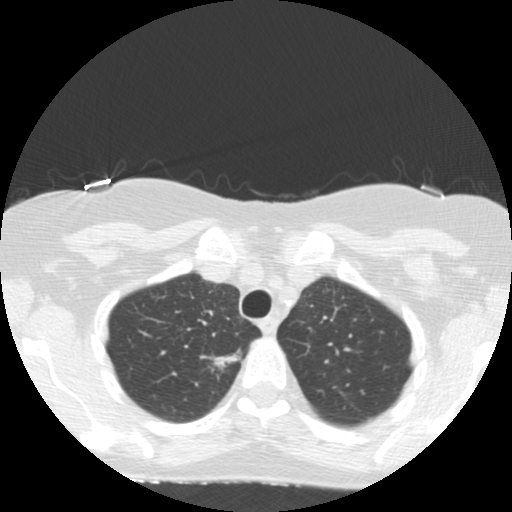
Low-dose screening chest CT, one axial slice; reconstruction kernel STANDARD; lung window (W 1500 / L -600 HU); 512 × 512 image matrix, field of view 300 × 300 mm.
Annotated regions visible in this slice (expert manual segmentation):
- lesion 1 (tumor, upper lobe of right lung): bounding box [x1, y1, x2, y2] px = [210, 354, 239, 370]